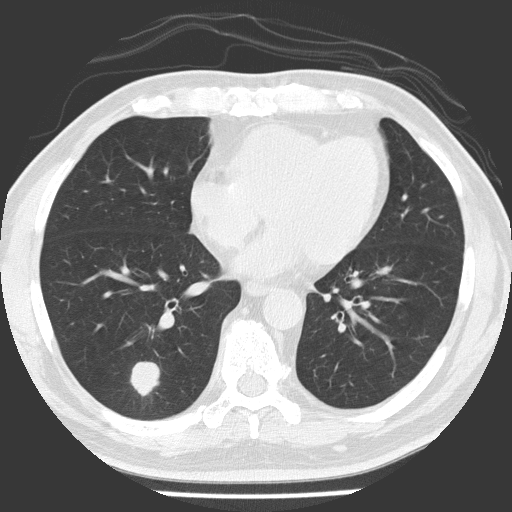
Low-dose screening chest CT, one axial slice. Slice 64 of 154 in the series (ordered by position). Reconstruction kernel FC51. 120 kVp. Lung window (W 1500 / L -600 HU). 2 mm slice thickness. 512 × 512 image matrix, field of view 311 × 311 mm.
Structures marked on this image (outlined manually by an expert reader):
- lesion 1 (tumor, lower lobe of right lung): bounding box <130,362,160,396> (left, top, right, bottom; pixels)